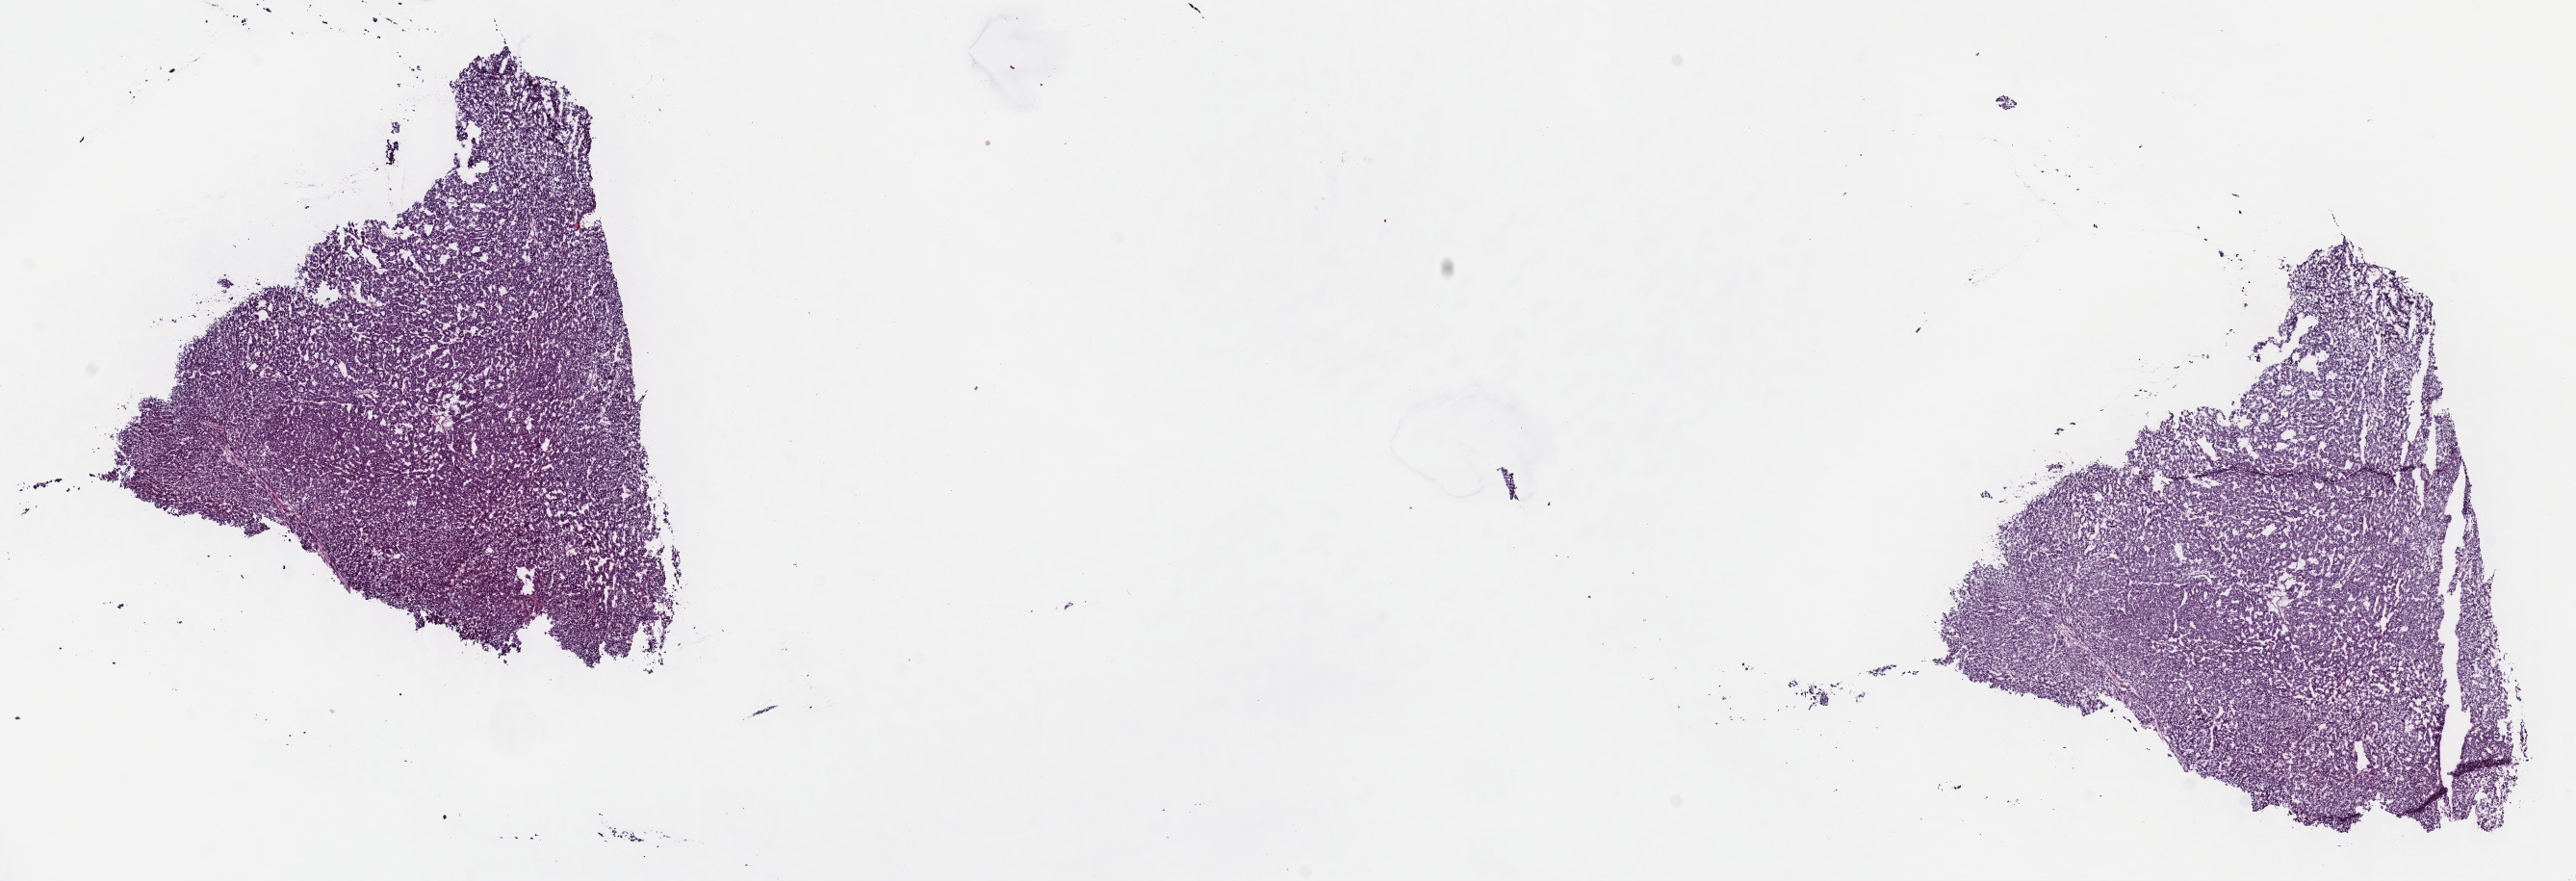
Whole-slide histology image, Hematoxylin and eosin (H&E) stained — shown as a low-resolution overview of the whole scanned area (about 21.6 x 7.4 mm), frozen section from the top of the tissue portion, primary tumour sample from the liver. Male, age 61 years at initial diagnosis. Composition of this section per pathologist review: tumour cells 100%, tumour nuclei 95%.
Diagnosis: Hepatocellular carcinoma, NOS.